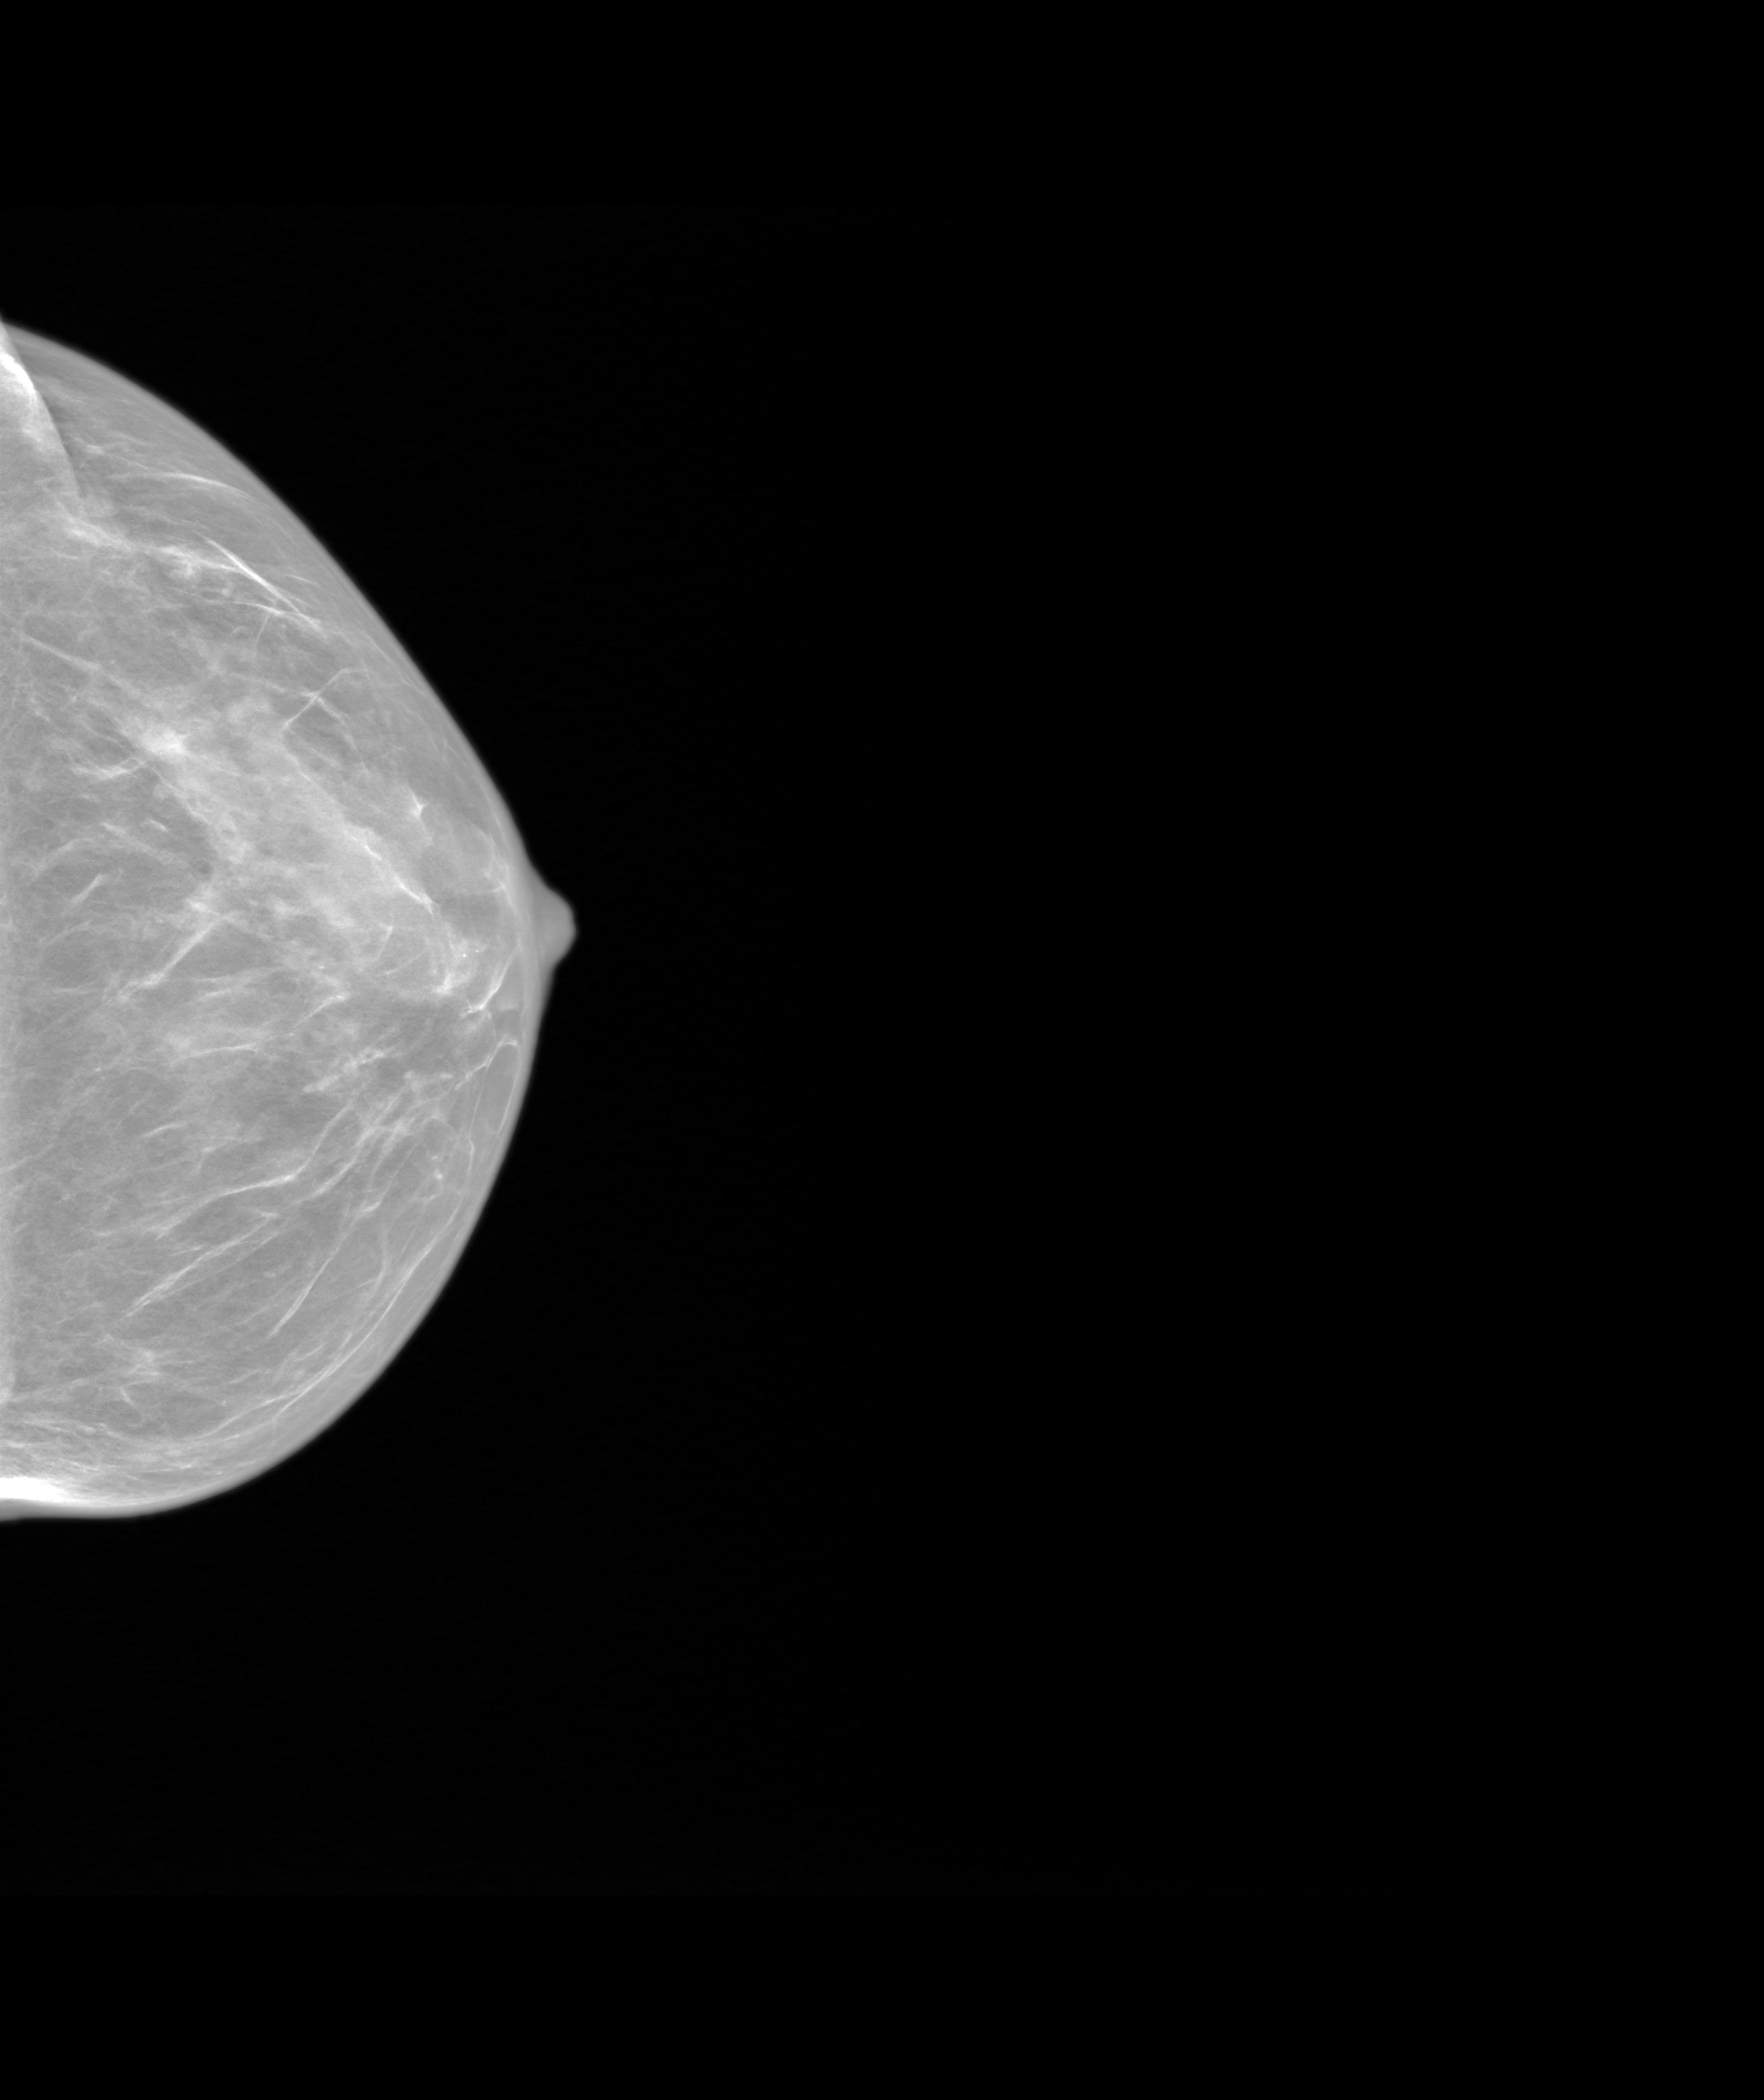
Annual screening mammography examination. Female patient, age 66 years.
Image type: synthesized 2-D view from tomosynthesis. Breast: left. Projection: cranio-caudal projection.